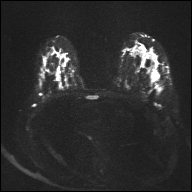
Breast MRI, one axial slice. Slice 22 of 32 in the series (ordered by position). Diffusion-weighted series; image 2 of 4 stored at this slice position (different b-values; order by instance number). 1.5 T. 4 mm slice thickness. 192 × 192 image matrix, field of view 360 × 360 mm. Female patient.
Outlined on this slice (outlined manually by an expert reader):
- tumour on diffusion-weighted imaging: bounding box [x1, y1, x2, y2] px = [157, 76, 159, 78]